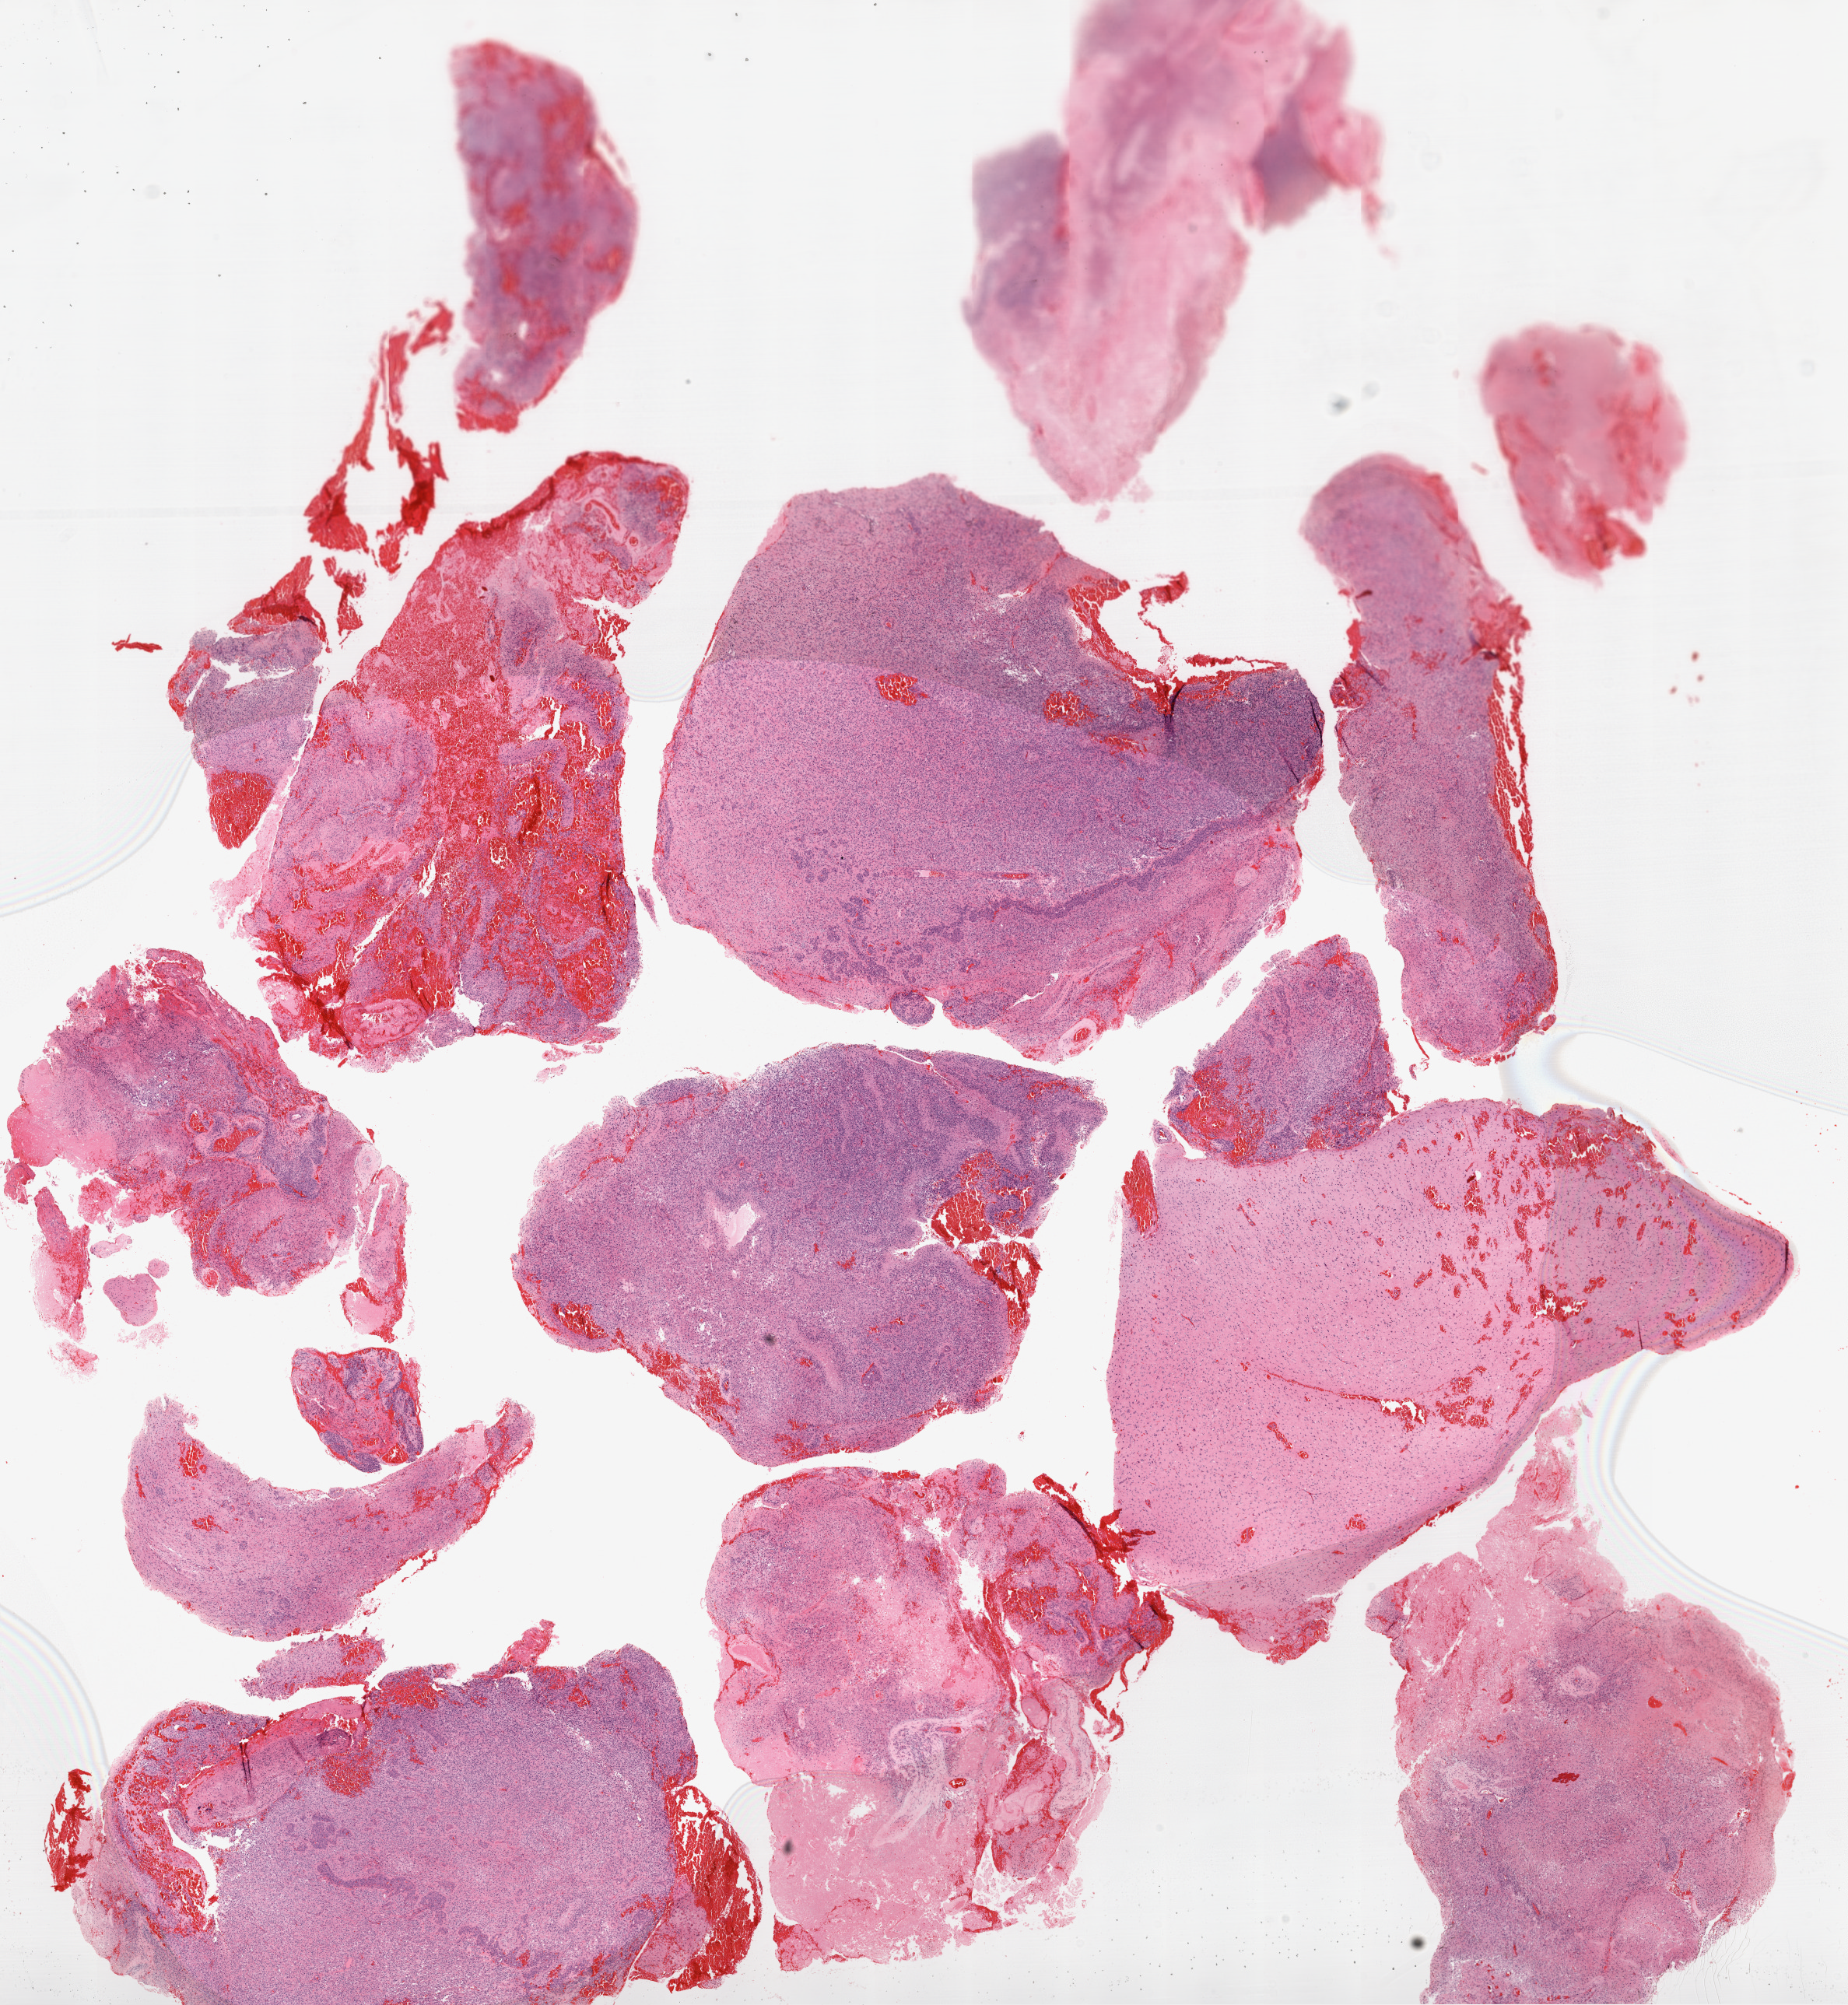
Digitized H&E tissue section (whole slide) — low-resolution overview of the scanned area, about 19.1 x 20.7 mm (slide scanned at 20x), FFPE section, sample: primary tumour, brain. Patient: male, age at initial diagnosis 51 years.
Histologic diagnosis: Glioblastoma.